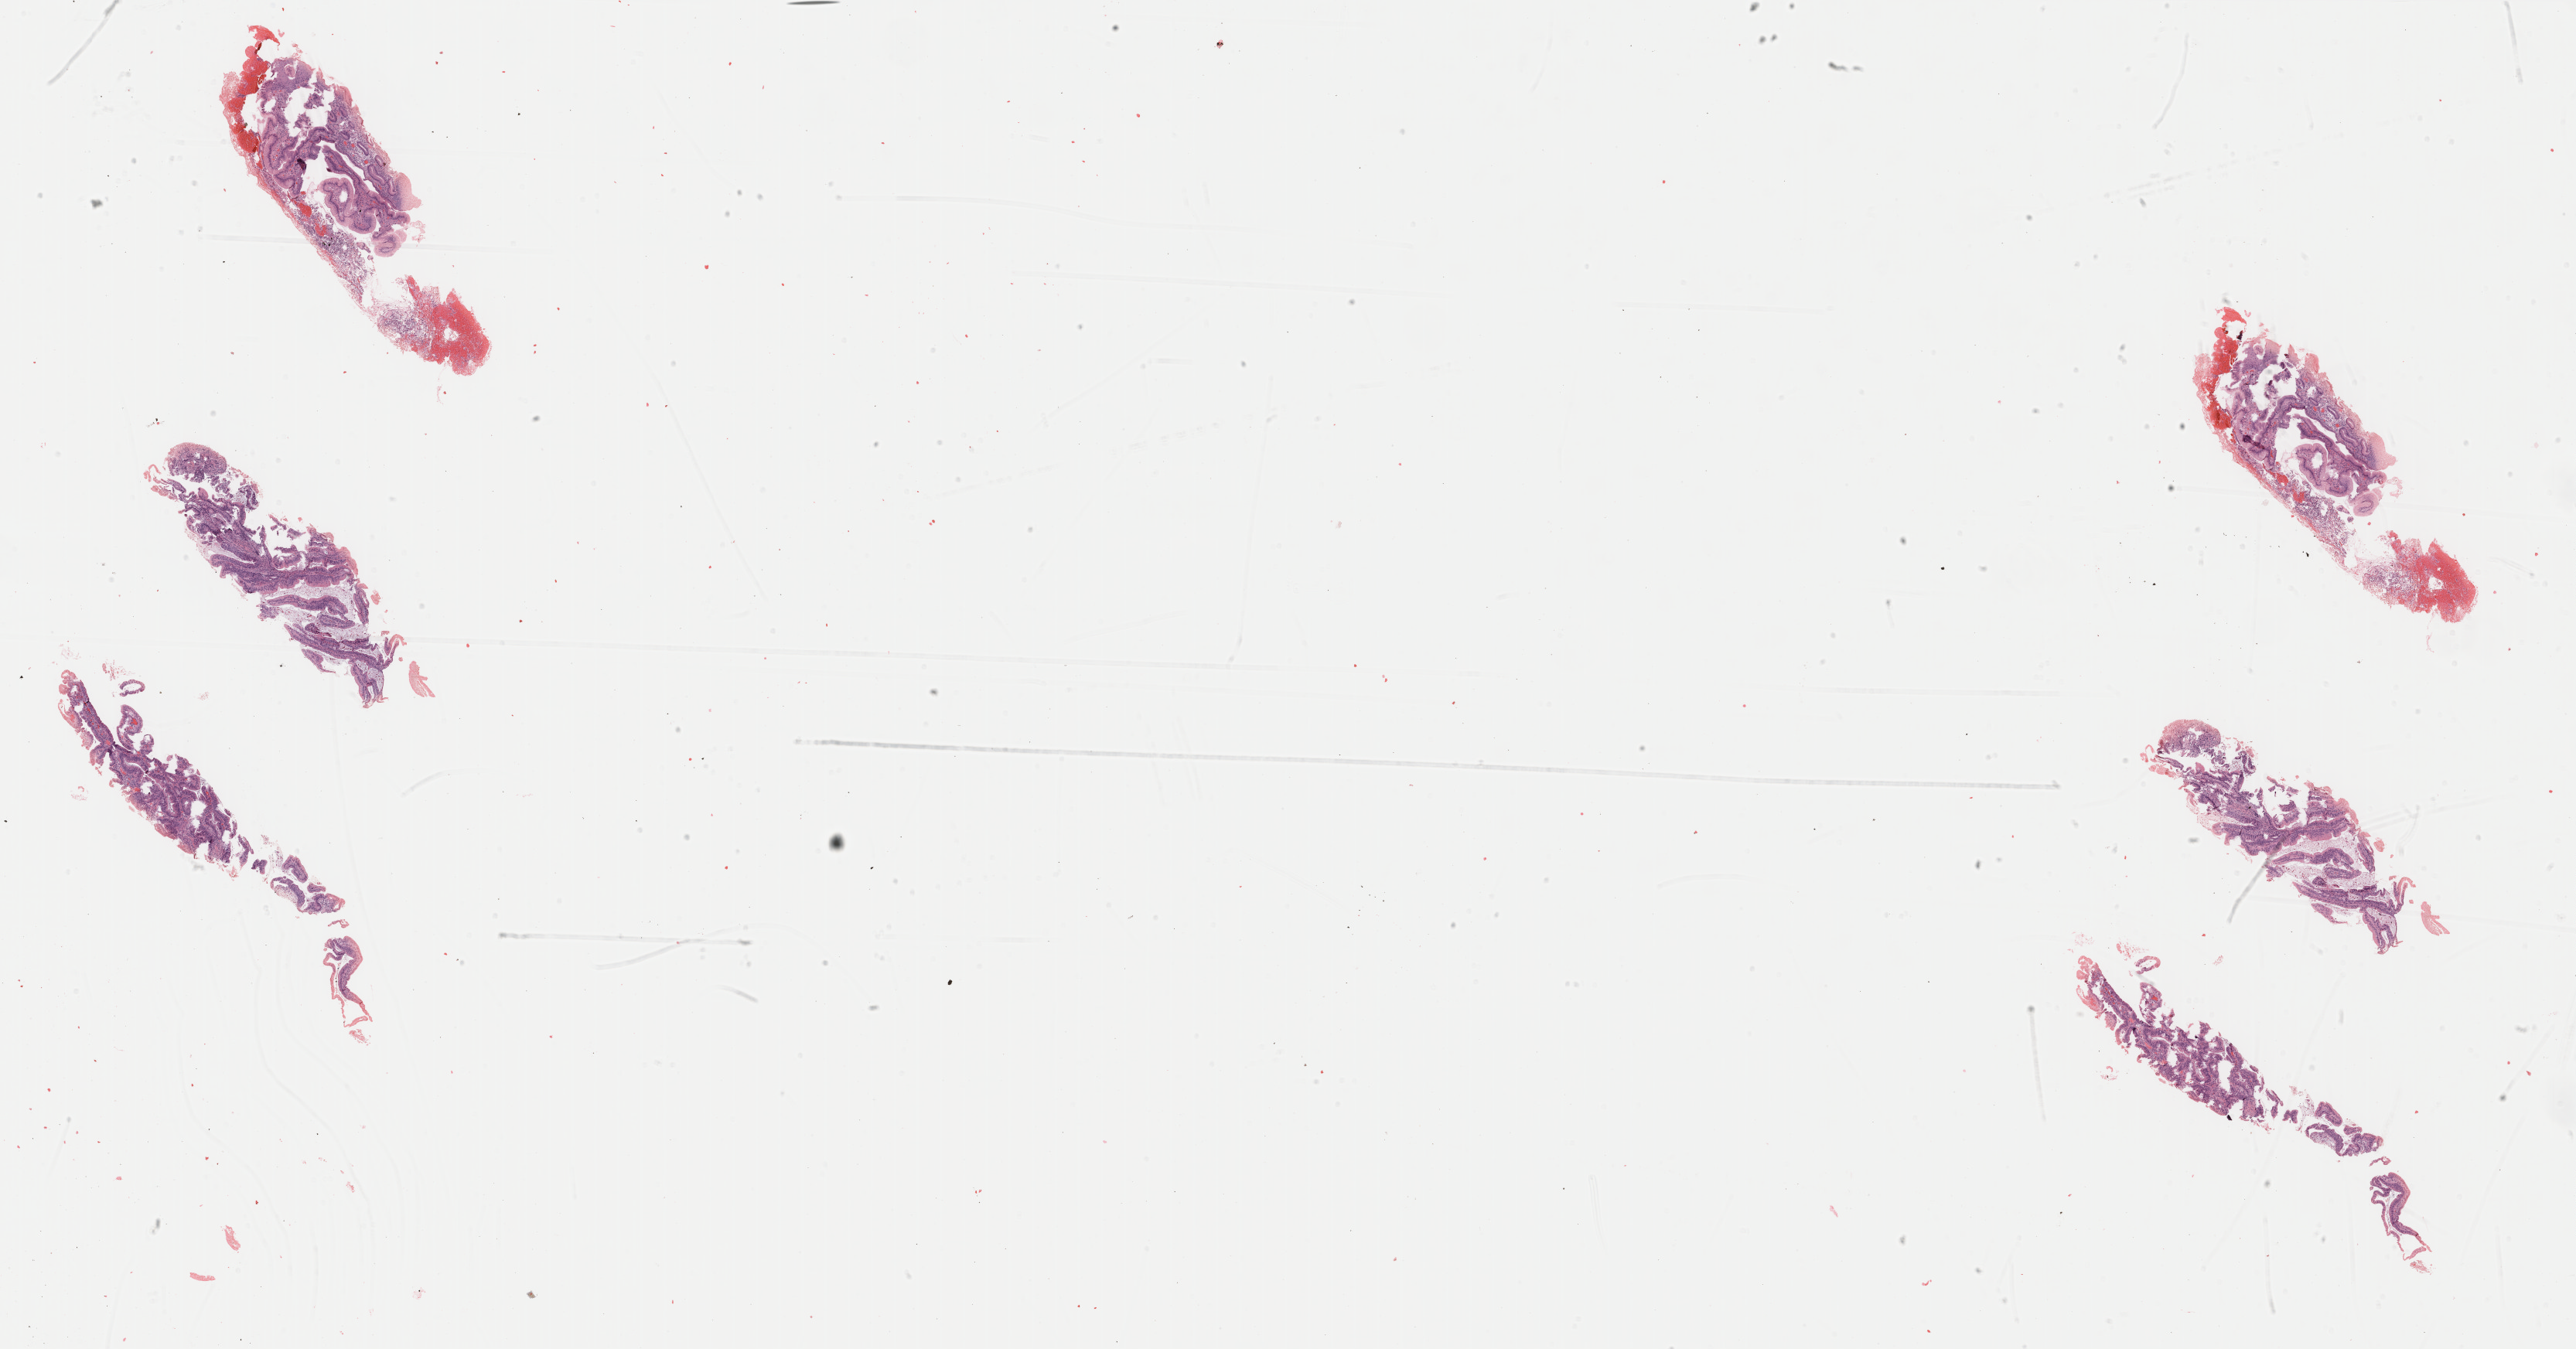
Whole-slide histology image, Hematoxylin and eosin (H&E) stained, a low-resolution overview of the entire scanned area, about 26.4 x 13.9 mm; formalin-fixed paraffin-embedded (FFPE) diagnostic section; primary tumour sample from the esophagus. Patient: male, age at initial diagnosis 54 years.
Histologic diagnosis: Adenocarcinoma, NOS.